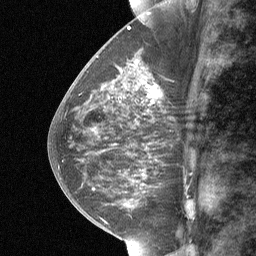
Breast MRI (dynamic contrast-enhanced), one sagittal slice. Position 31 of 64 along the scan axis. Dynamic contrast-enhanced study with each time point stored as its own series, time point 2 of 3 at this slice position (early post-contrast, ordered by acquisition time). 1.5 T. TE 4.8 ms, TR 27 ms. 256 × 256 image matrix, field of view 180 × 180 mm. Female patient, age 59 years. From the clinical record (not read from this slice): setting: breast cancer imaged before/during neoadjuvant chemotherapy; receptor status: triple-negative.
Outlined on this slice (semi-automatic segmentation, software-assisted and operator-edited):
- analysis volume of interest (the breast-tissue region the enhancement analysis was run in; not a lesion): bounding box [x1, y1, x2, y2] px = [127, 66, 165, 118]
- tumour enhancement mask (voxels above the 90 % enhancement threshold inside the analysis volume of interest): [154, 88, 159, 97]